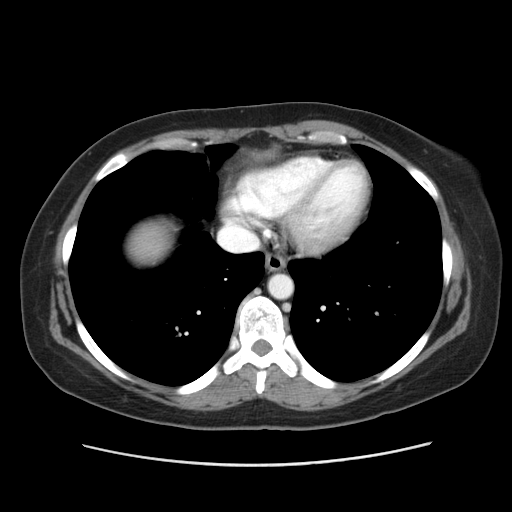
Contrast-enhanced abdominal CT, one axial slice; reconstruction kernel STANDARD; 120 kVp; intravenous contrast given; soft-tissue window (W 400 / L 40 HU); 5 mm slice thickness; 512 × 512 image matrix. Female patient, age 48 years. From the clinical record (not read from this slice): diagnosis: colorectal cancer liver metastases, imaged before liver resection; multiple liver metastases: yes; largest metastasis: 4.5 cm.
Outlined on this slice (outlined manually by an expert reader):
- liver: bounding box <133,226,168,250> (left, top, right, bottom; pixels)